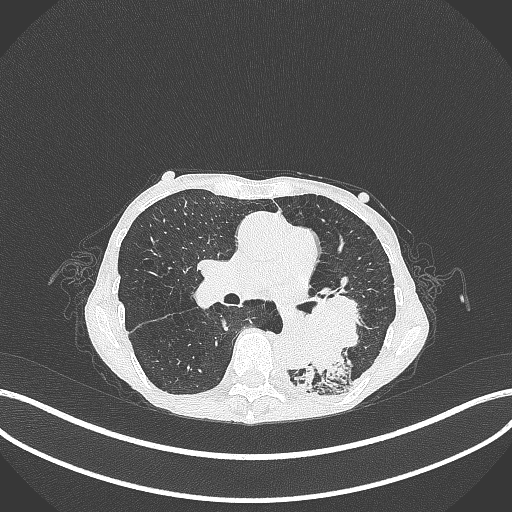
Chest CT, one axial slice; slice 147 of 347 in the series (ordered by position); reconstruction kernel B70f; 120 kVp; lung window (W 1500 / L -600 HU); 1 mm slice thickness; 512 × 512 image matrix. Female patient, age 70 years. Case-level facts recorded for this patient, not image findings: clinical TNM (as recorded): T3 N0 M0.
Structures marked on this image (bounding box drawn by a radiologist):
- lung tumour (recorded histology: small cell carcinoma): box from (x=289, y=282) to (x=364, y=375) px